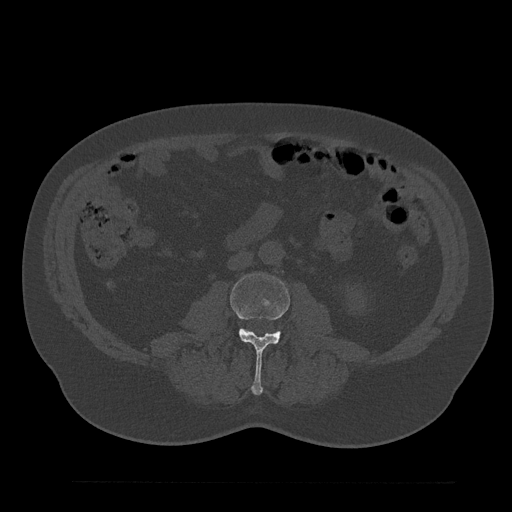
CT including the spine, one axial slice; position 24 of 797 along the scan axis; reconstruction kernel Br40s/3; bone window (W 1800 / L 400 HU); 0.5 mm slice thickness; 512 × 512 image matrix, field of view 430 × 430 mm. Male patient, age 61 years. From the clinical record (not read from this slice): primary cancer: prostate.
Outlined on this slice (semi-automatic segmentation, software-assisted and operator-edited):
- L3 vertebra: box from (x=230, y=273) to (x=290, y=395) px